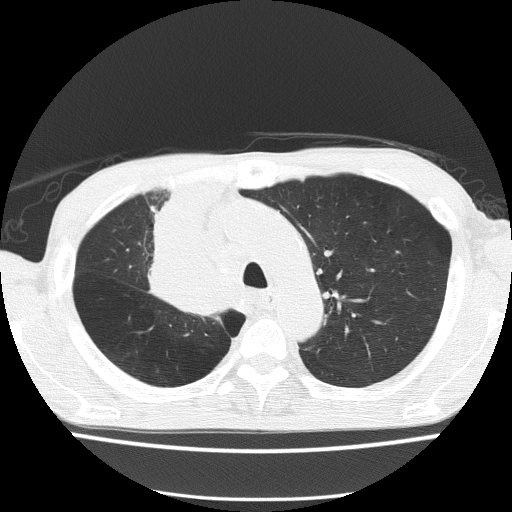
Chest CT (low-dose screening protocol), one axial image. First (baseline) screen. Lung window (W 1500 / L -600 HU). 2 mm slice thickness. Lung (sharp) reconstruction kernel (FC51). Male, age 59 years at enrolment.
Expert reader's lesion annotation, box from (x=134, y=233) to (x=237, y=325) px. The screening reader recorded 5 non-calcified nodules or masses ≥4 mm on this exam (left upper lobe, left upper lobe, left upper lobe, right middle lobe, right lower lobe); which of them this box marks is not recorded.